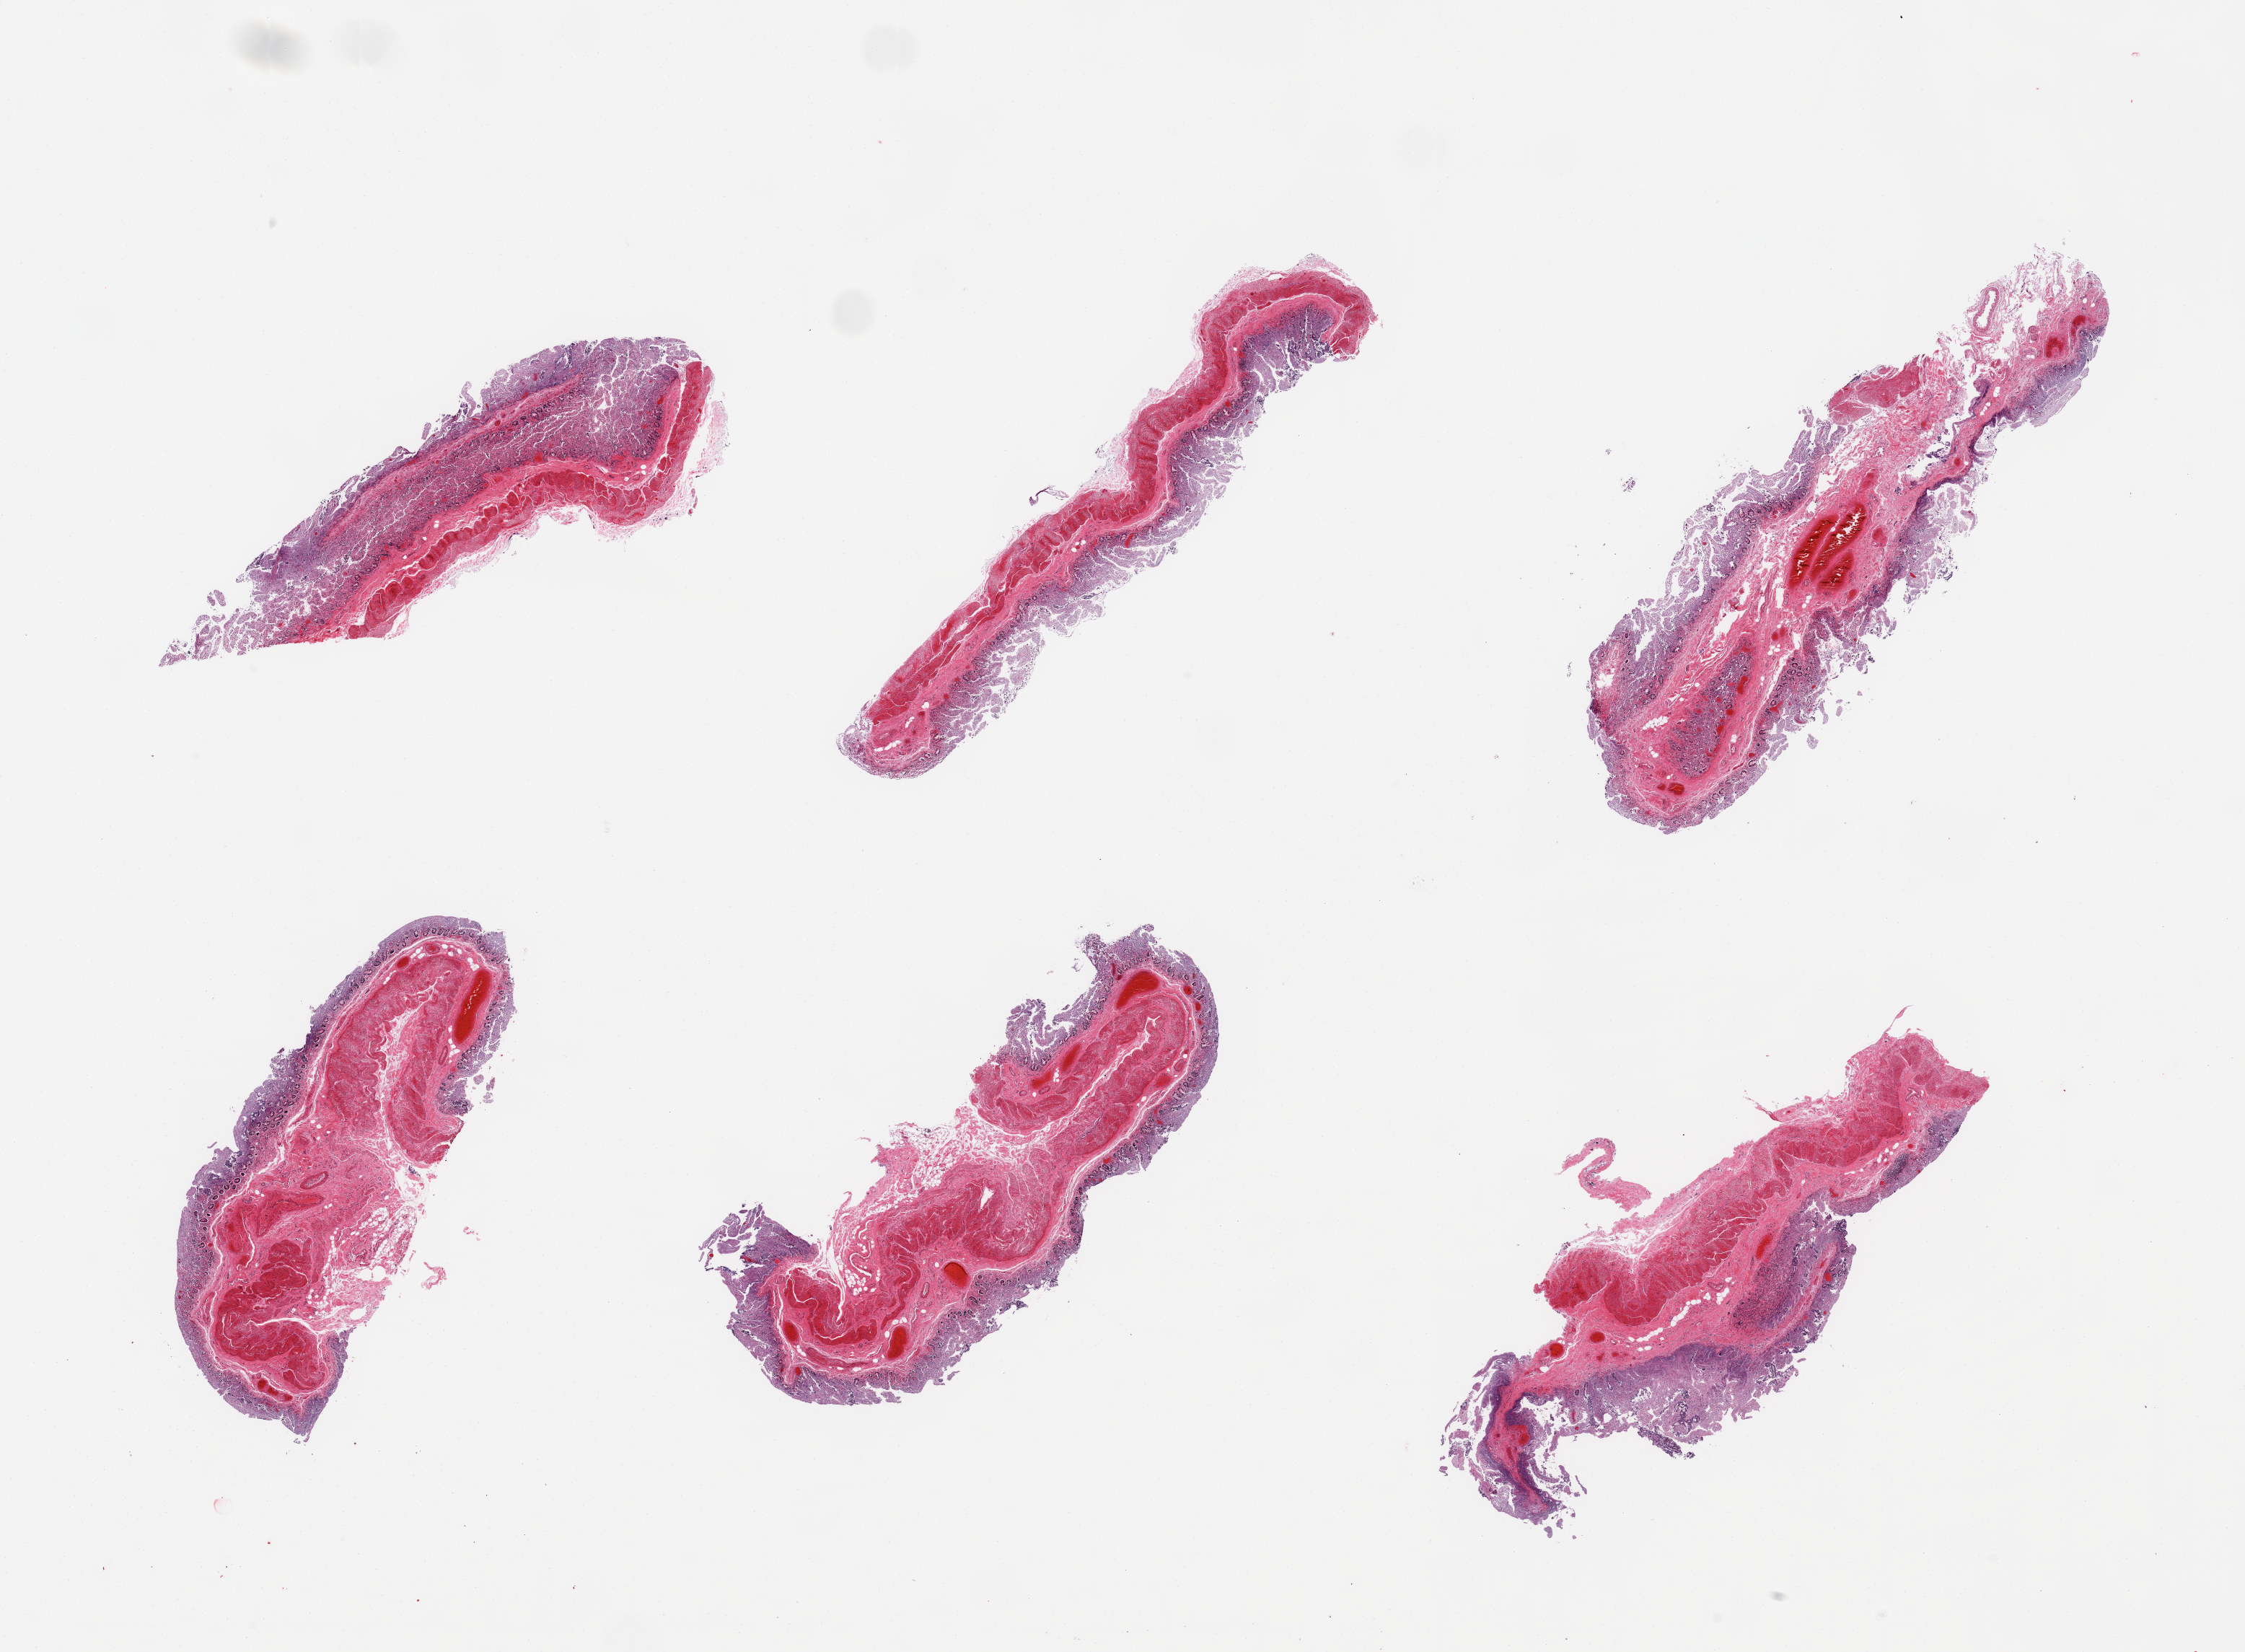
Whole-slide image, haematoxylin and eosin stain, shown as a low-resolution overview of the whole scanned area (about 24.6 x 18.1 mm). PAXgene-fixed paraffin-embedded (PFPE) section. Target tissue: transverse colon. Tissue donor sample. Donor sex: male.
* reviewer comment on this tissue sample: 6 pieces; glands autolyzed, muscle intact